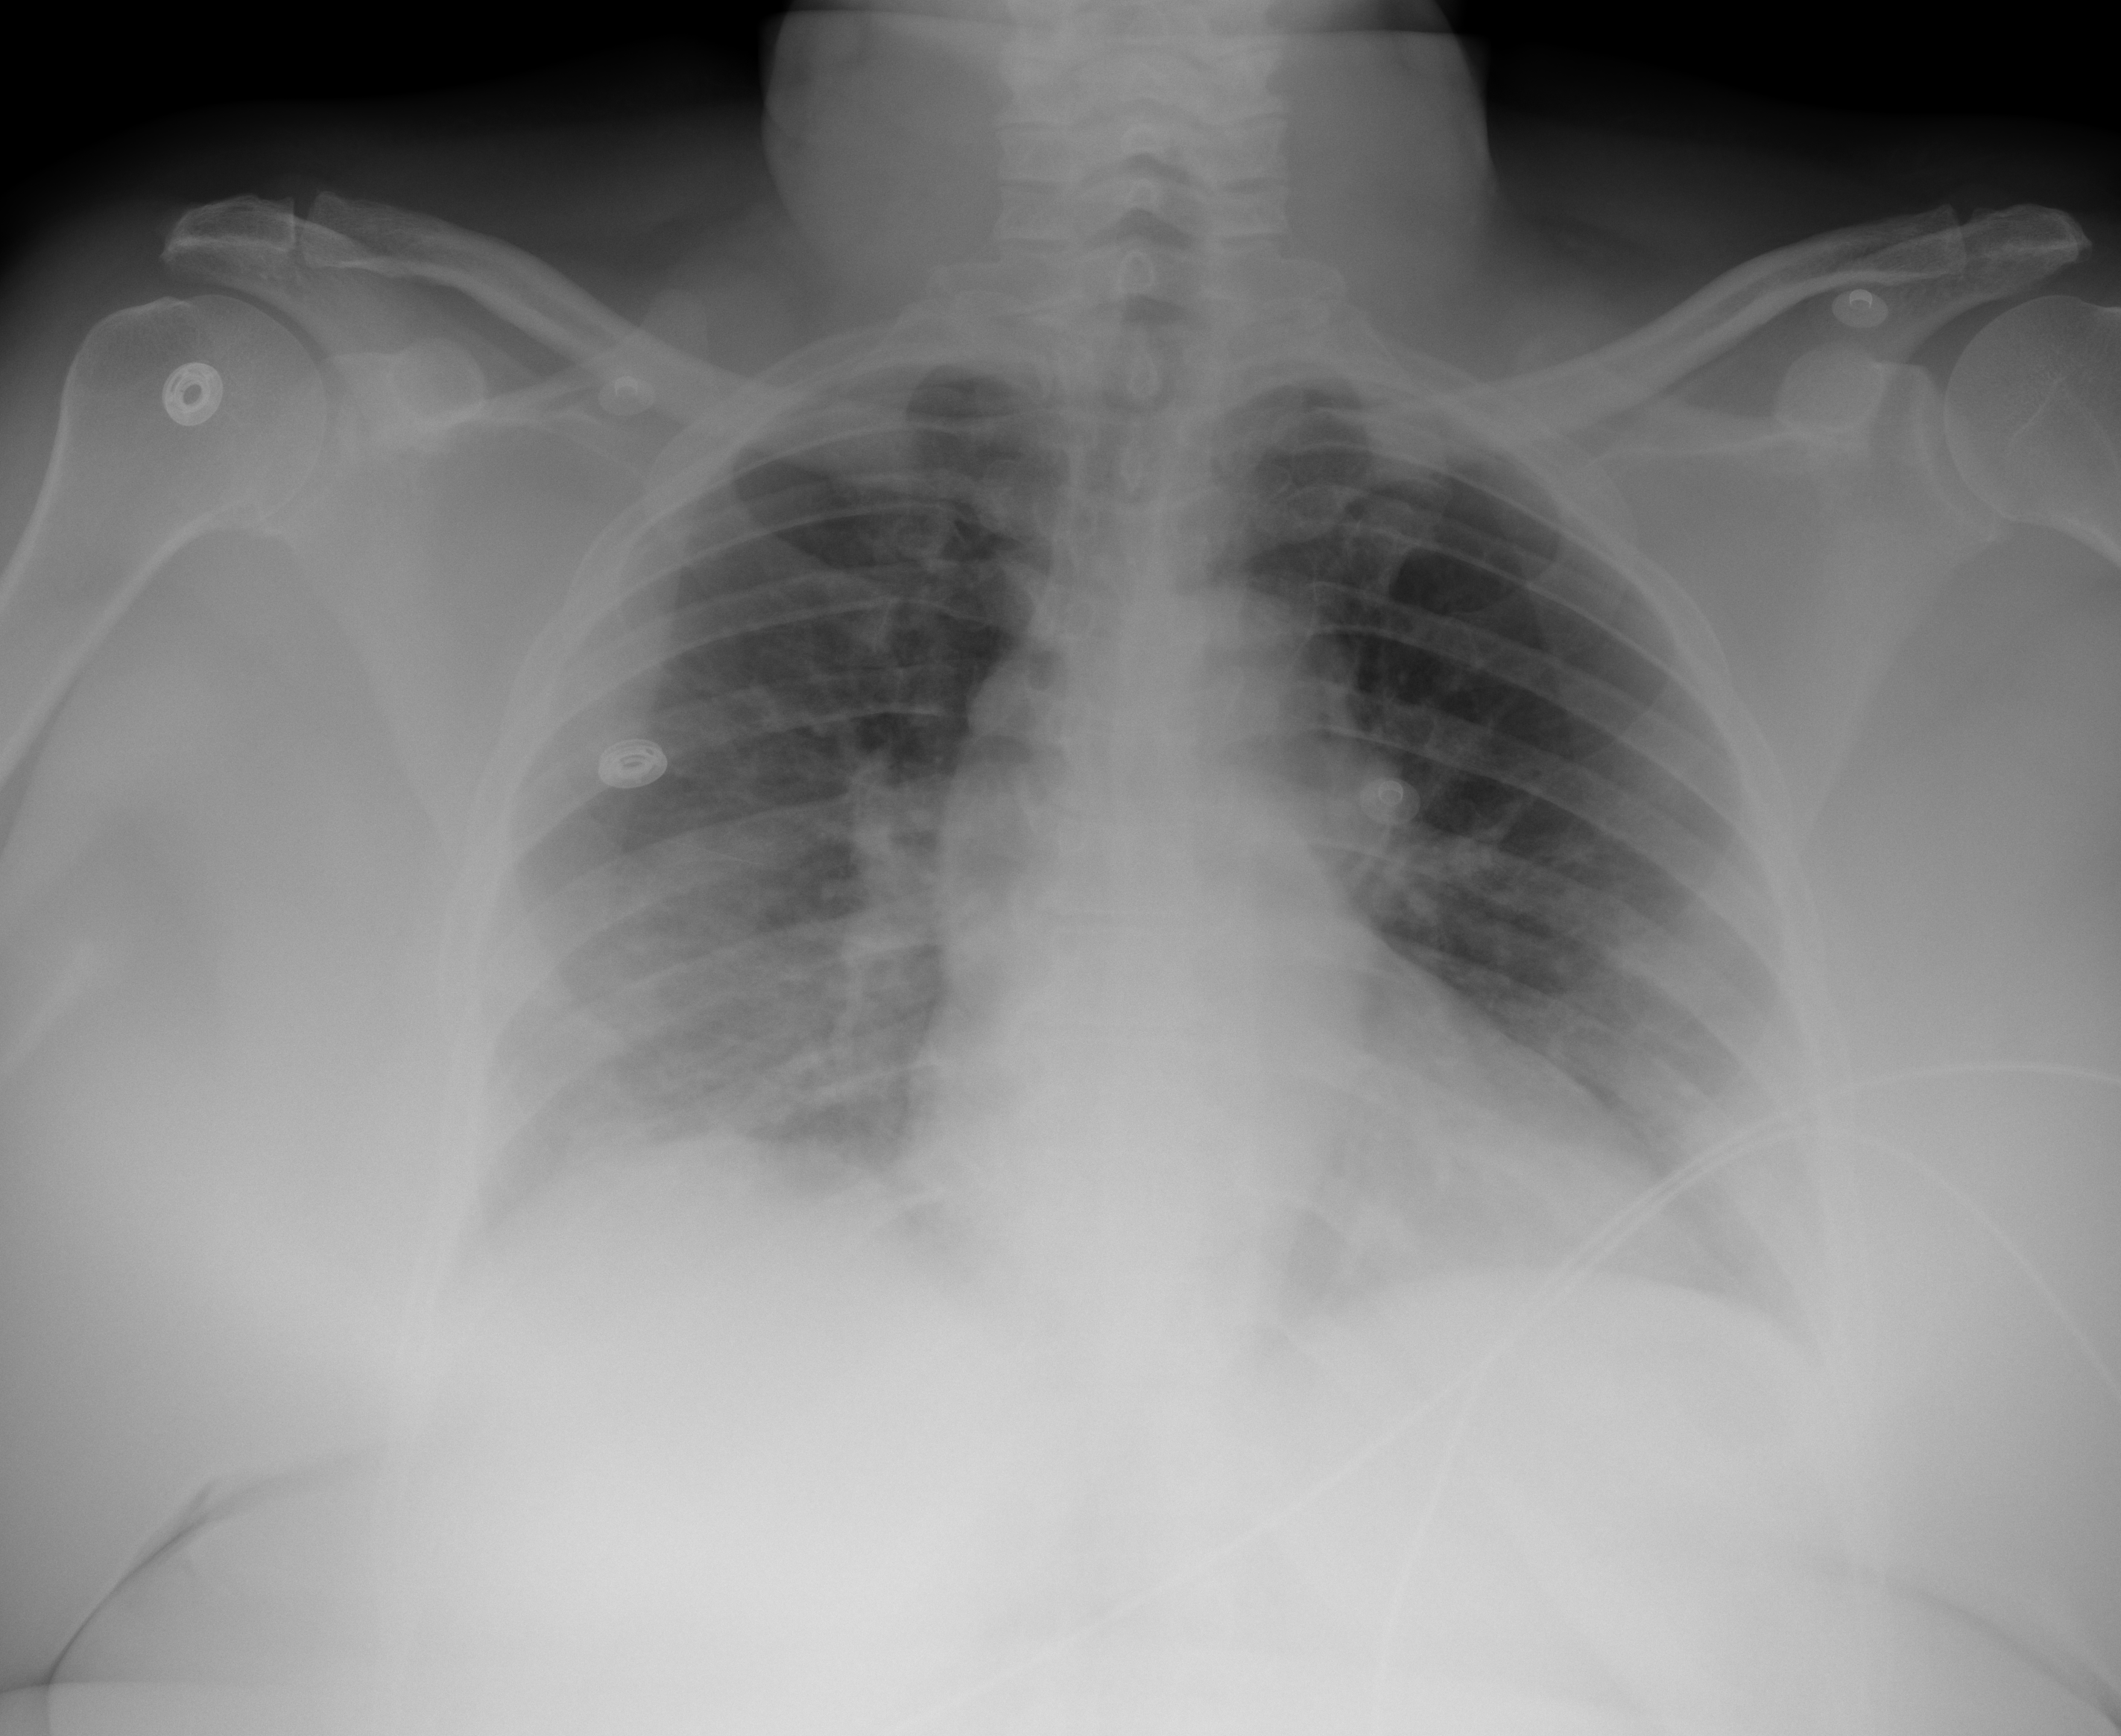
Portable chest radiograph, AP projection. Female patient, age 60 years; COVID-19 (test-positive).
Key findings recorded by the radiologist: Ground-glass opacities in bilateral lower lobes slightly more pronounced on the right side with additional right lung base.